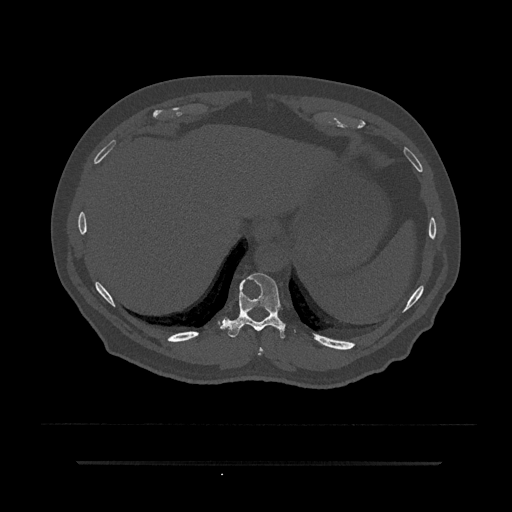
CT including the spine, one axial slice. Position 328 of 797 along the scan axis. Bone window (W 1800 / L 400 HU). 0.5 mm slice thickness. 512 × 512 image matrix. Male patient, age 59 years. Case-level facts recorded for this patient, not image findings: primary cancer: bile ducts; vertebrae with lytic lesions (as recorded): T10.
Annotated regions visible in this slice (semi-automatic segmentation, software-assisted and operator-edited):
- T10 vertebra: bounding box <220,273,296,339> (left, top, right, bottom; pixels)
- T9 vertebra: <258,347,263,355>